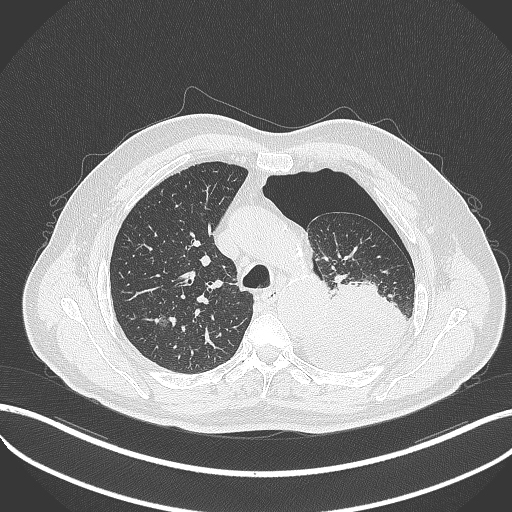
Chest CT, one axial slice. Position 368 of 464 along the scan axis. Reconstruction kernel B70f. Lung window (W 1500 / L -600 HU). 1 mm slice thickness. 512 × 512 image matrix. Patient: male, 76 years. Case-level facts recorded for this patient, not image findings: clinical TNM (as recorded): T3 N0 M1b.
Outlined on this slice (bounding box drawn by a radiologist):
- lung tumour (recorded histology: adenocarcinoma): box from (x=300, y=275) to (x=407, y=377) px